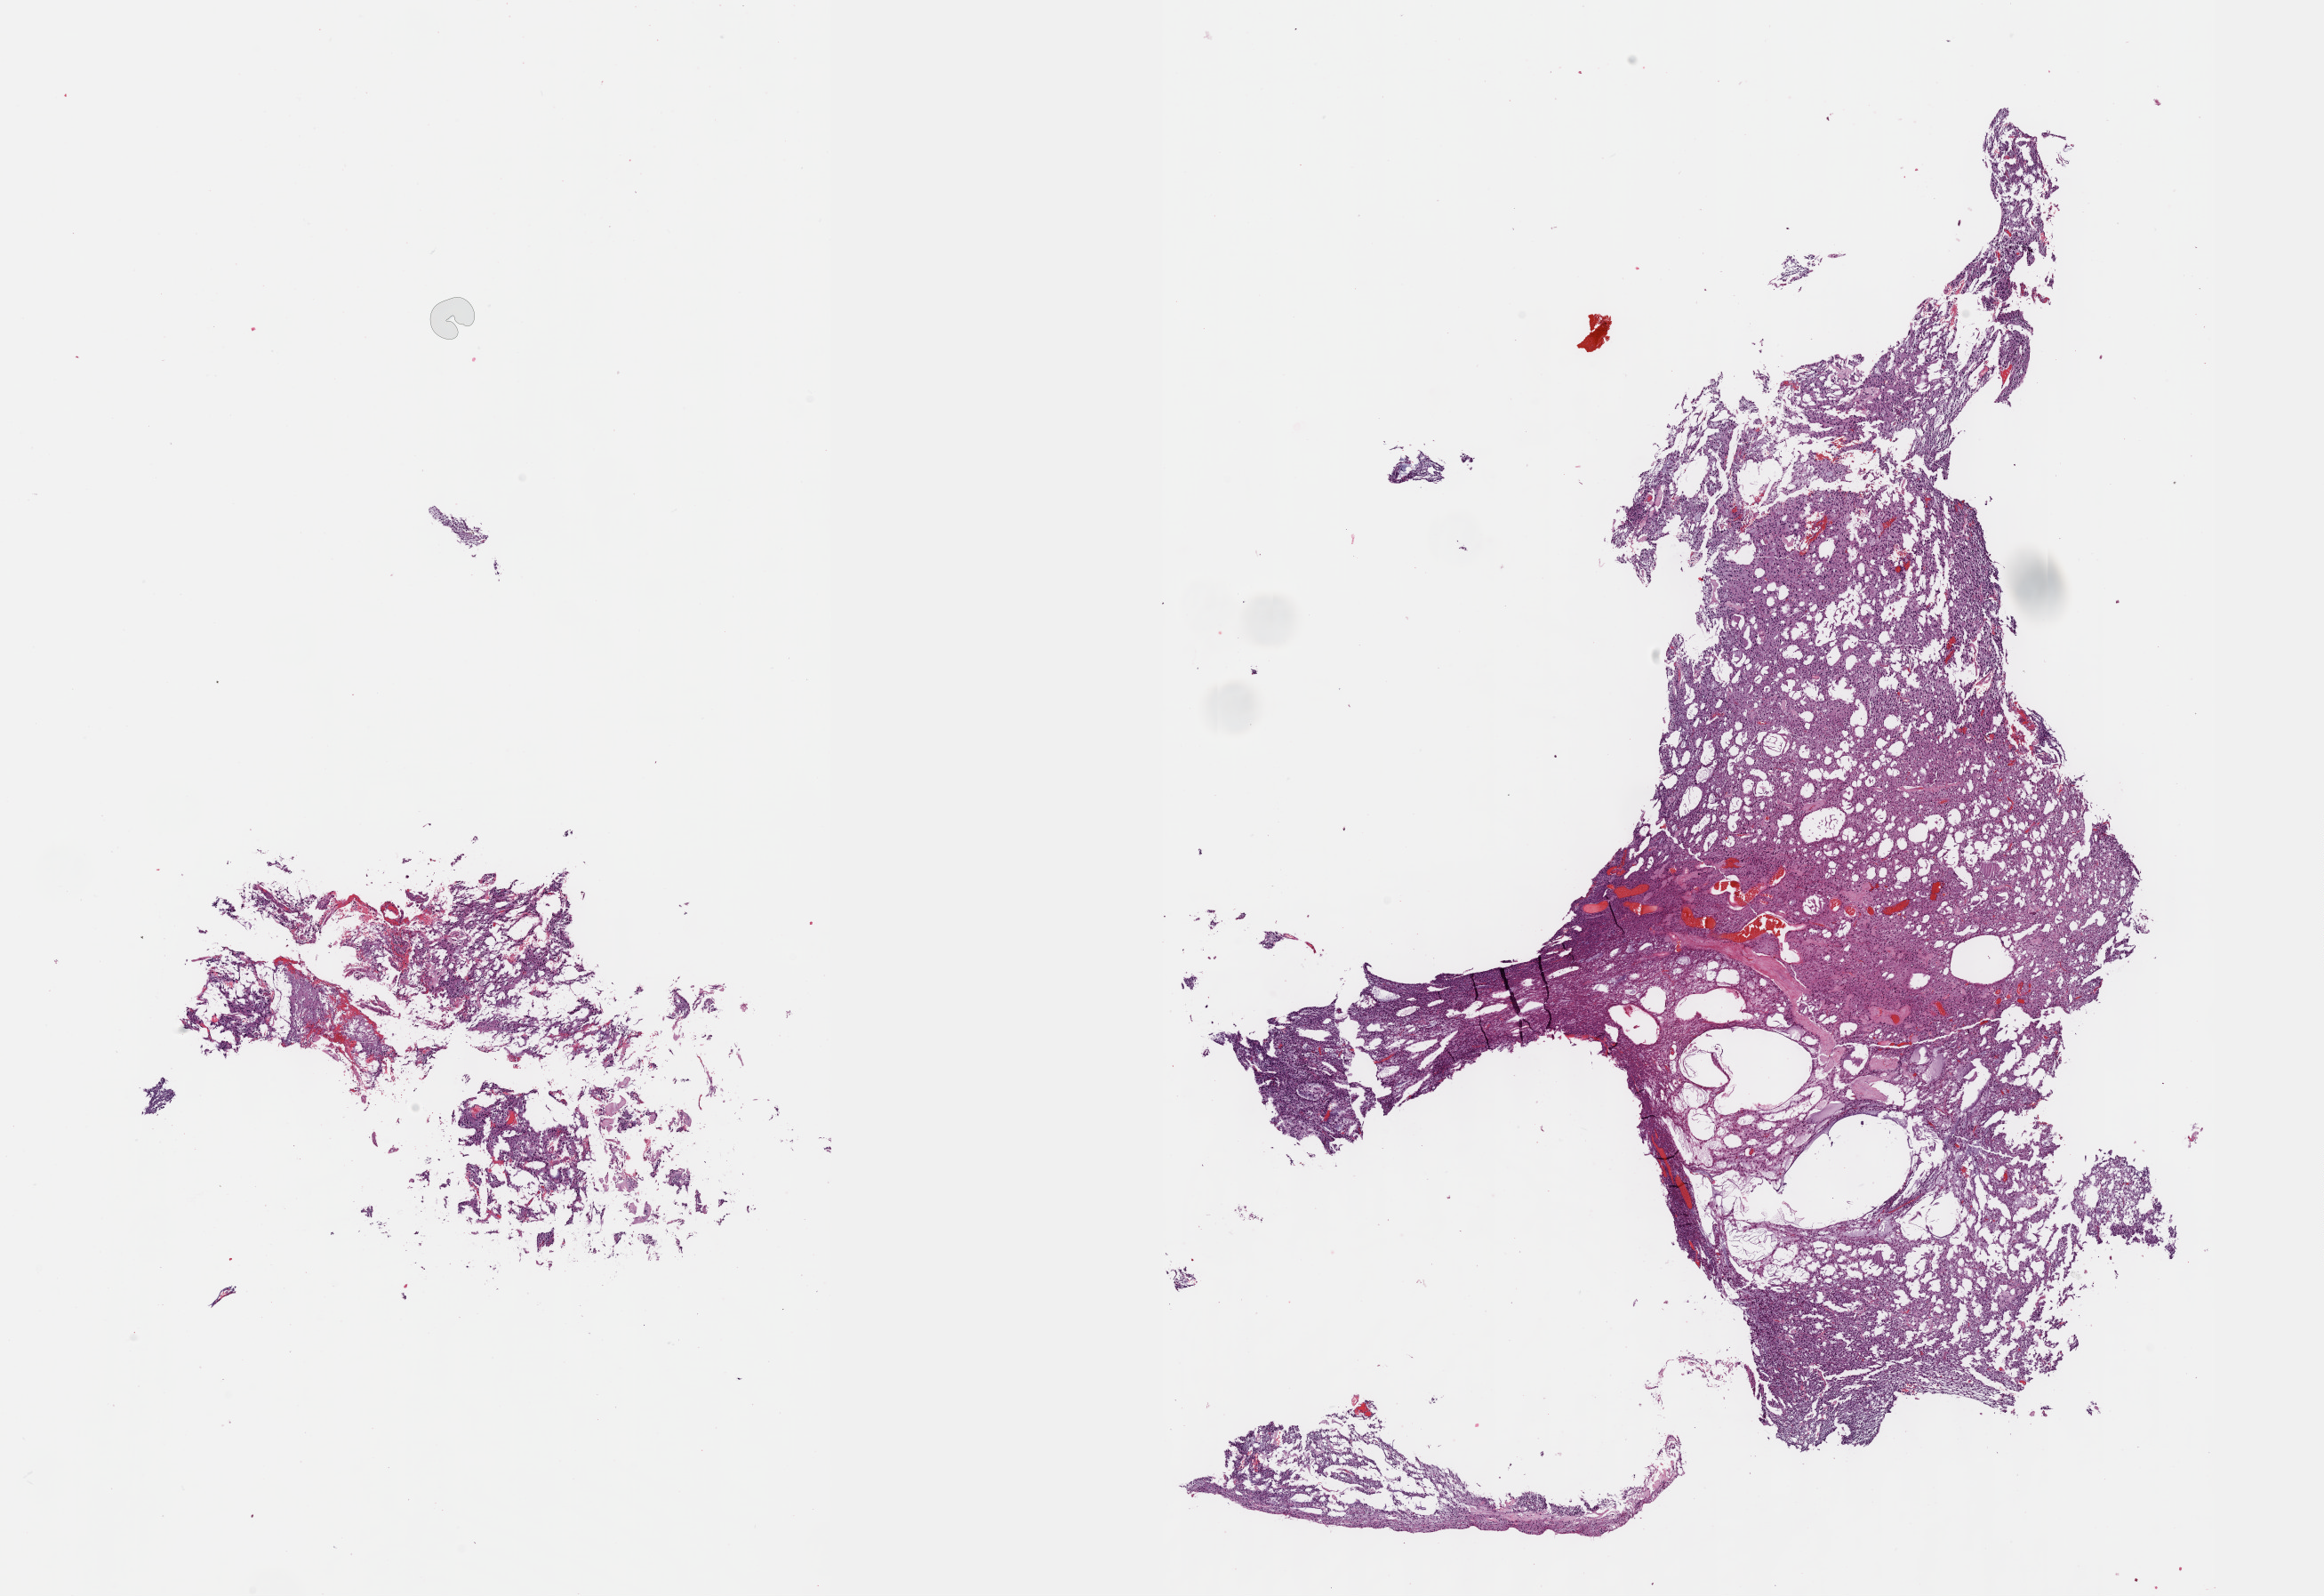
Whole-slide histology image, H&E — shown as a low-resolution overview of the whole scanned area (about 21.1 x 14.5 mm). Formalin-fixed paraffin-embedded (FFPE) diagnostic section. Brain, primary tumour sample. Female, age 51 years at initial diagnosis. Histologic grade: G2 (moderately differentiated).
Histologic diagnosis: Oligodendroglioma, NOS (cerebrum).